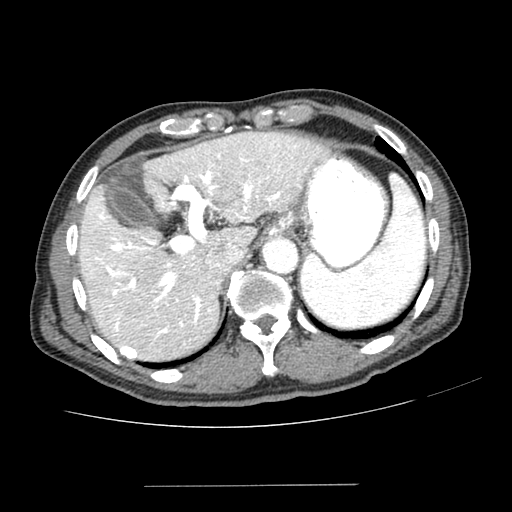
Contrast-enhanced abdominal CT (liver protocol), one axial slice. Position 165 of 187 along the scan axis. 100 kVp. One of 2 acquisitions stored at this slice position. Soft-tissue window (W 400 / L 40 HU). 512 × 512 image matrix. Case-level facts recorded for this patient, not image findings: diagnosis: hepatocellular carcinoma (patient treated with transarterial chemoembolisation; whether this scan precedes or follows treatment is not stated here); TNM stage (as recorded): Stage-I; Child-Pugh class: A; tumour nodularity: uninodular.
Structures marked on this image (semi-automatically segmented with operator editing):
- liver parenchyma outside the tumour (the mass and vessels are separate outlines, so this box may not span the whole liver): bounding box [x1, y1, x2, y2] px = [78, 132, 328, 360]
- liver vessels: [94, 141, 306, 337]